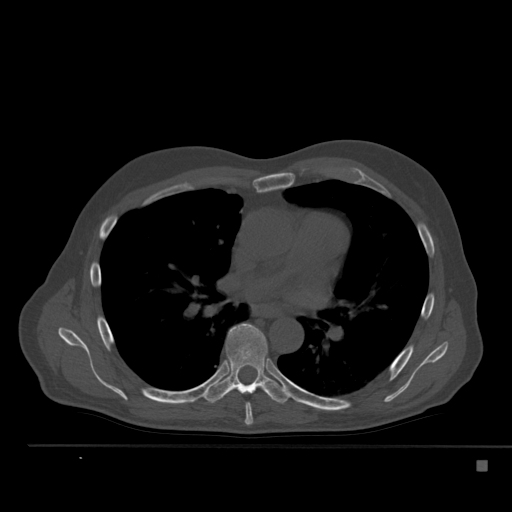
CT including the spine, one axial slice. Position 334 of 517 along the scan axis. 120 kVp. Bone window (W 1800 / L 400 HU). 1.5 mm slice thickness. 512 × 512 image matrix, field of view 408 × 408 mm. Male patient, age 70 years. Case-level facts recorded for this patient, not image findings: primary cancer: renal.
Annotated regions visible in this slice (semi-automatically segmented with operator editing):
- T6 vertebra: box from (x=244, y=403) to (x=253, y=425) px
- T7 vertebra: (x=203, y=324)–(x=292, y=404)